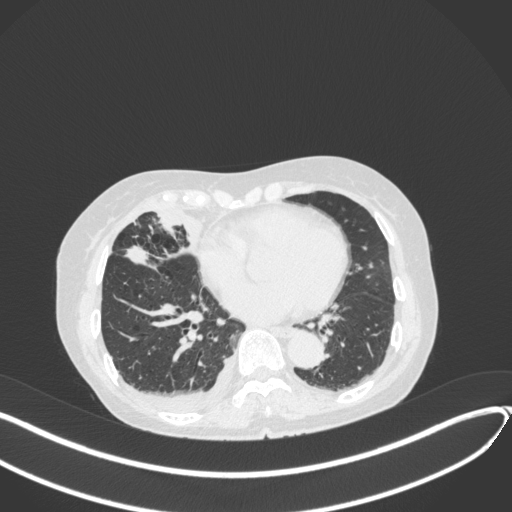
Chest CT, one axial slice. Reconstruction kernel B31f. 120 kVp. Lung window (W 1500 / L -600 HU). 512 × 512 image matrix. Female patient, age 75 years. Case-level facts recorded for this patient, not image findings: clinical TNM (as recorded): T2a N3 M0.
Annotated regions visible in this slice (bounding box drawn by a radiologist):
- lung tumour (recorded histology: adenocarcinoma): box from (x=123, y=244) to (x=151, y=271) px